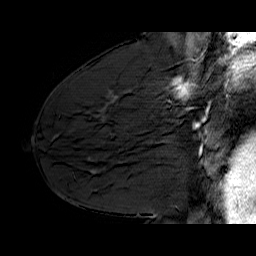
Breast MRI (dynamic contrast-enhanced), one sagittal slice. Slice 34 of 60 in the series (ordered by position). Dynamic contrast-enhanced series, time point 2 of 6 at this slice position (early post-contrast). 1.5 T. TE 6.4 ms, TR 32.9 ms. 4 mm slice thickness. 256 × 256 image matrix, field of view 200 × 200 mm. Female patient. From the clinical record (not read from this slice): setting: breast cancer imaged before/during neoadjuvant chemotherapy; receptor status: HER2-positive.
Structures marked on this image (semi-automatically segmented with operator editing):
- analysis volume of interest (the breast-tissue region the enhancement analysis was run in; not a lesion): box from (x=134, y=62) to (x=210, y=128) px
- tumour enhancement mask (voxels above the 100 % enhancement threshold inside the analysis volume of interest): (x=172, y=79)–(x=194, y=99)